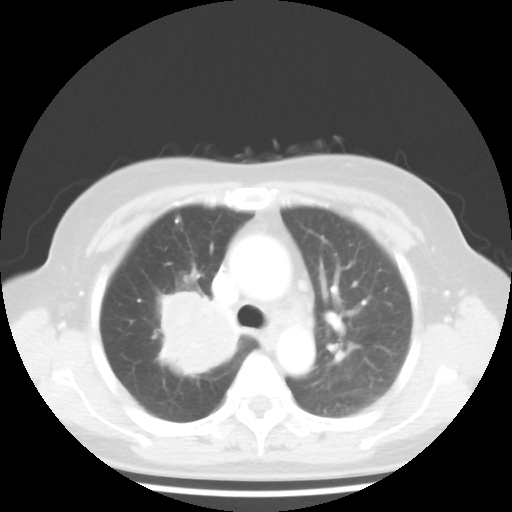
Chest CT, one axial slice. Position 30 of 44 along the scan axis. 100 kVp. Lung window (W 1500 / L -600 HU). 512 × 512 image matrix, field of view 316 × 316 mm. Patient: female, 62 years. From the clinical record (not read from this slice): clinical TNM (as recorded): T3 N0 M0; histopathological grade: G3.
Outlined on this slice (bounding box drawn by a radiologist):
- lung tumour (recorded histology: small cell carcinoma): box from (x=148, y=283) to (x=250, y=383) px